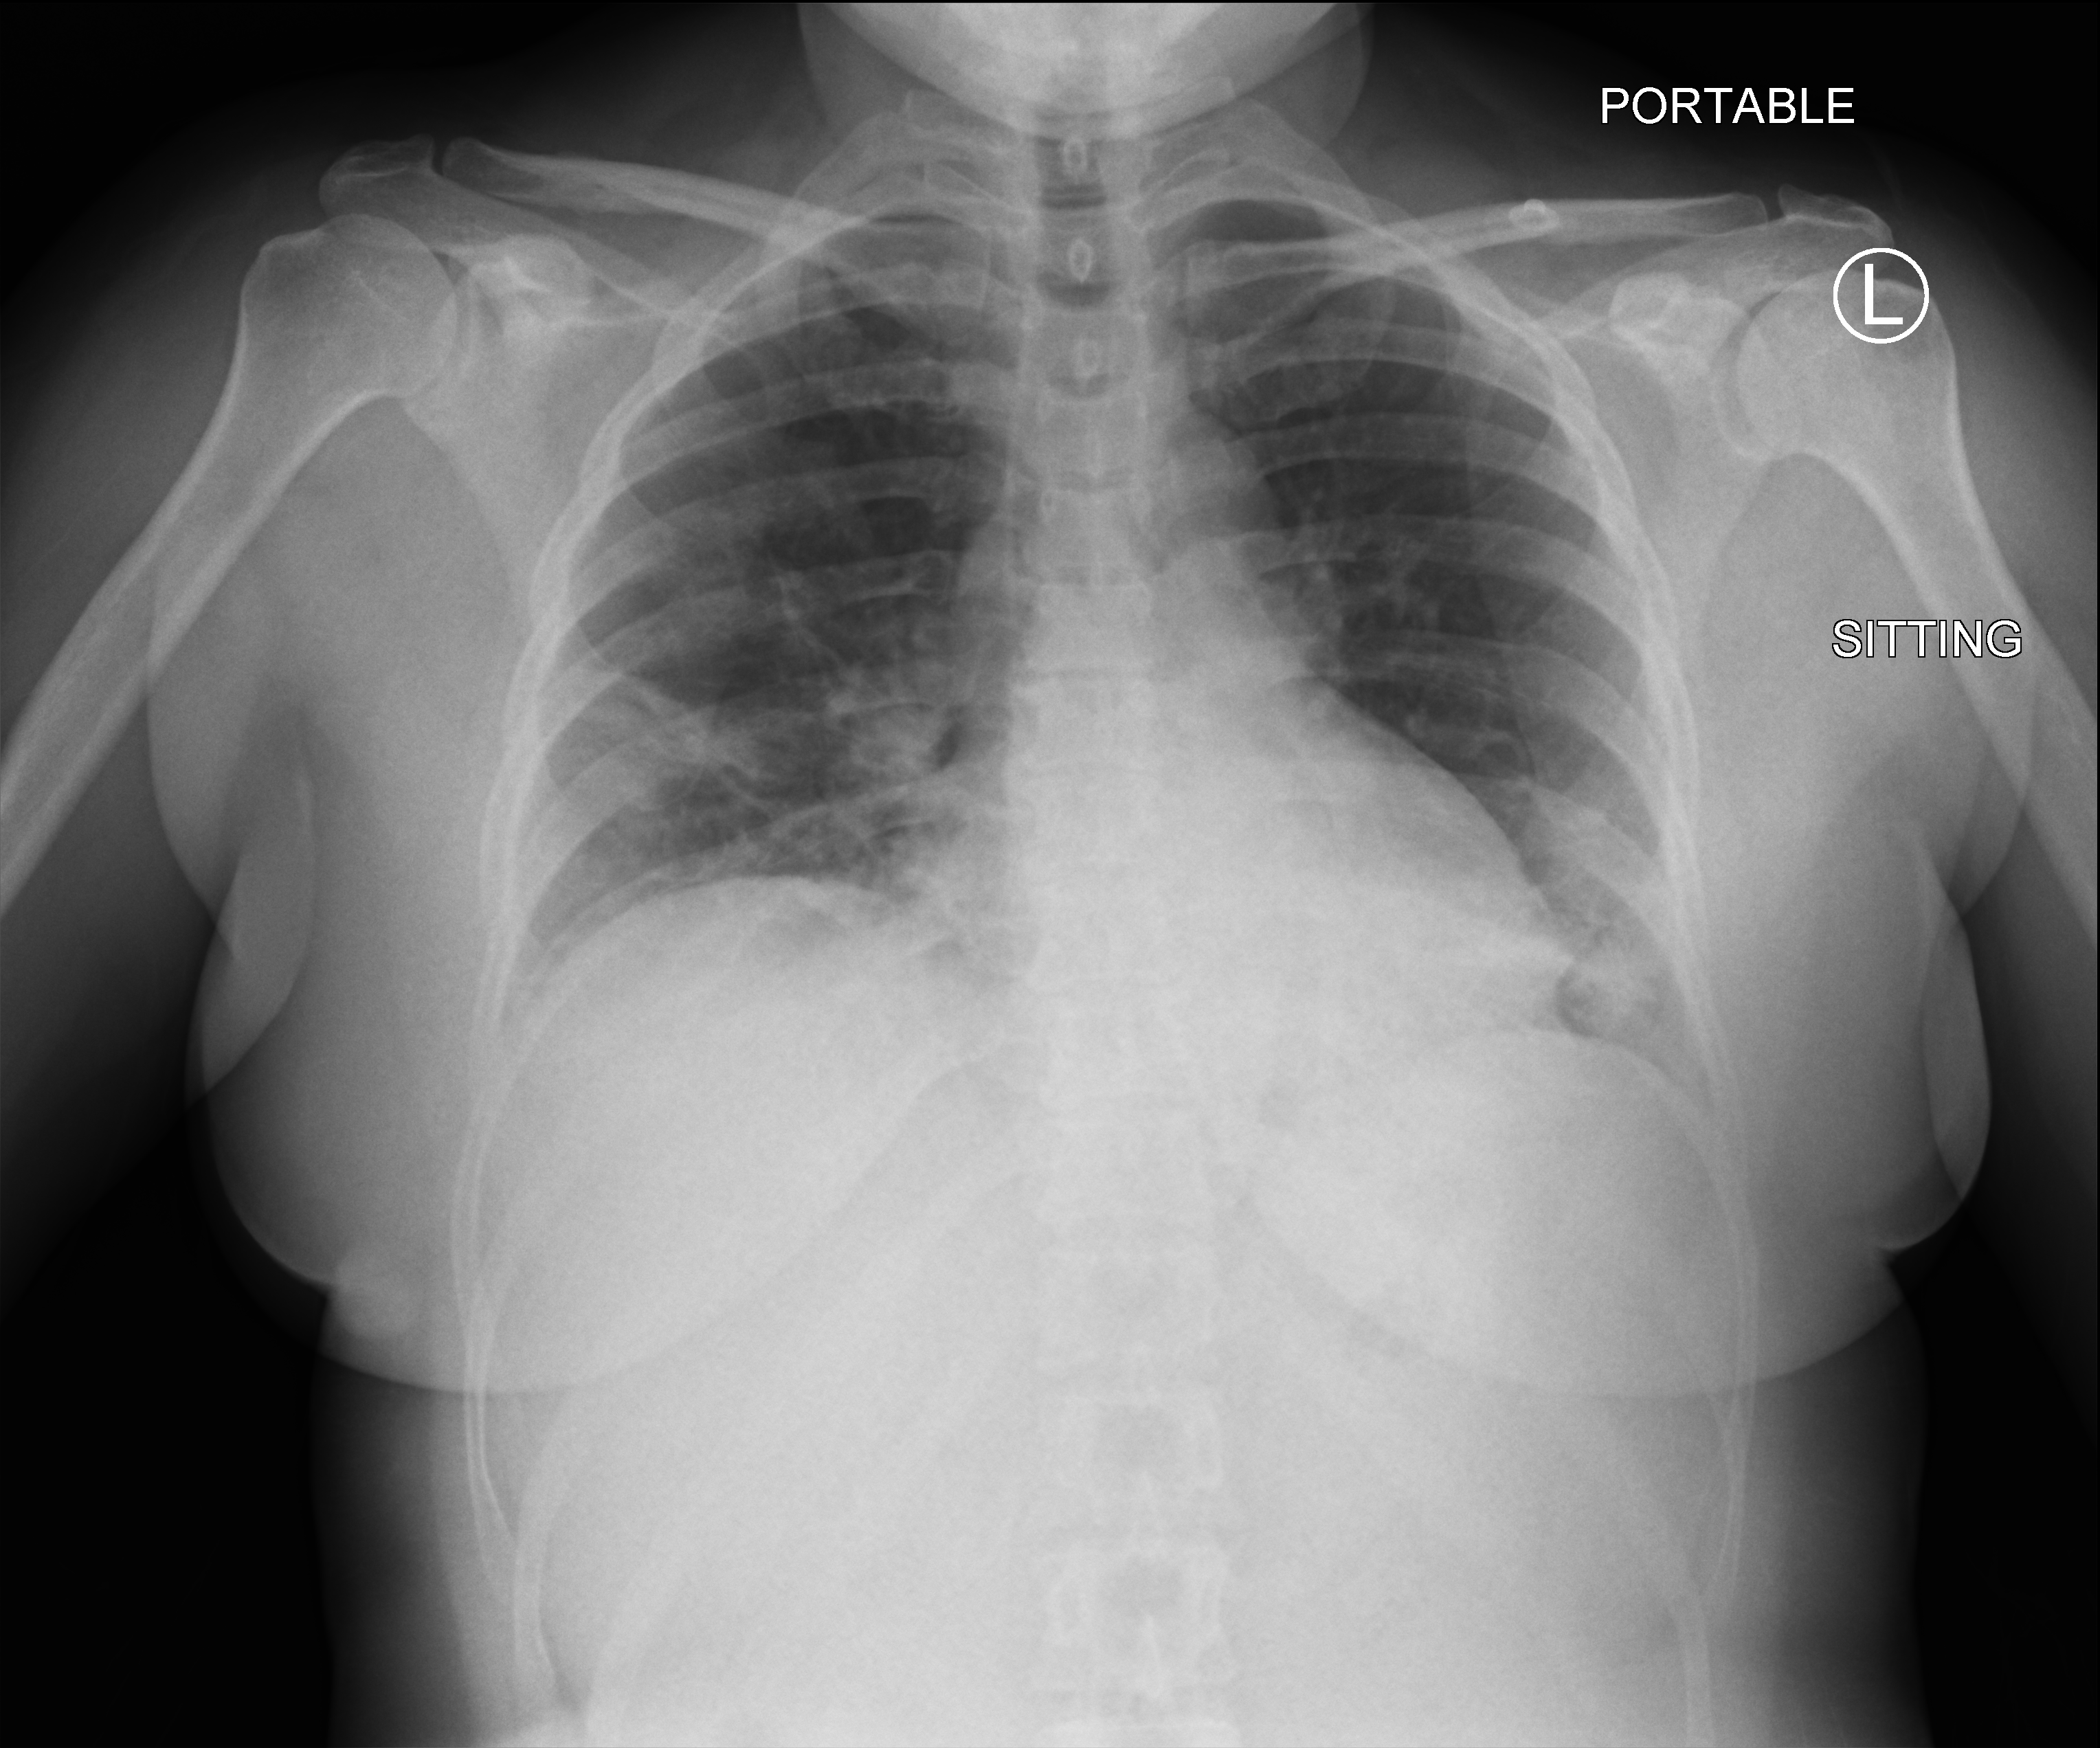
Chest X-ray (portable); anteroposterior (AP) projection. Patient hospitalised with COVID-19; female, aged 18–59 years.
Admission-level facts for this patient (not findings on this image; timing relative to this image not recorded):
- mechanically ventilated during this hospital stay: no
- admitted to intensive care during this hospital stay: no